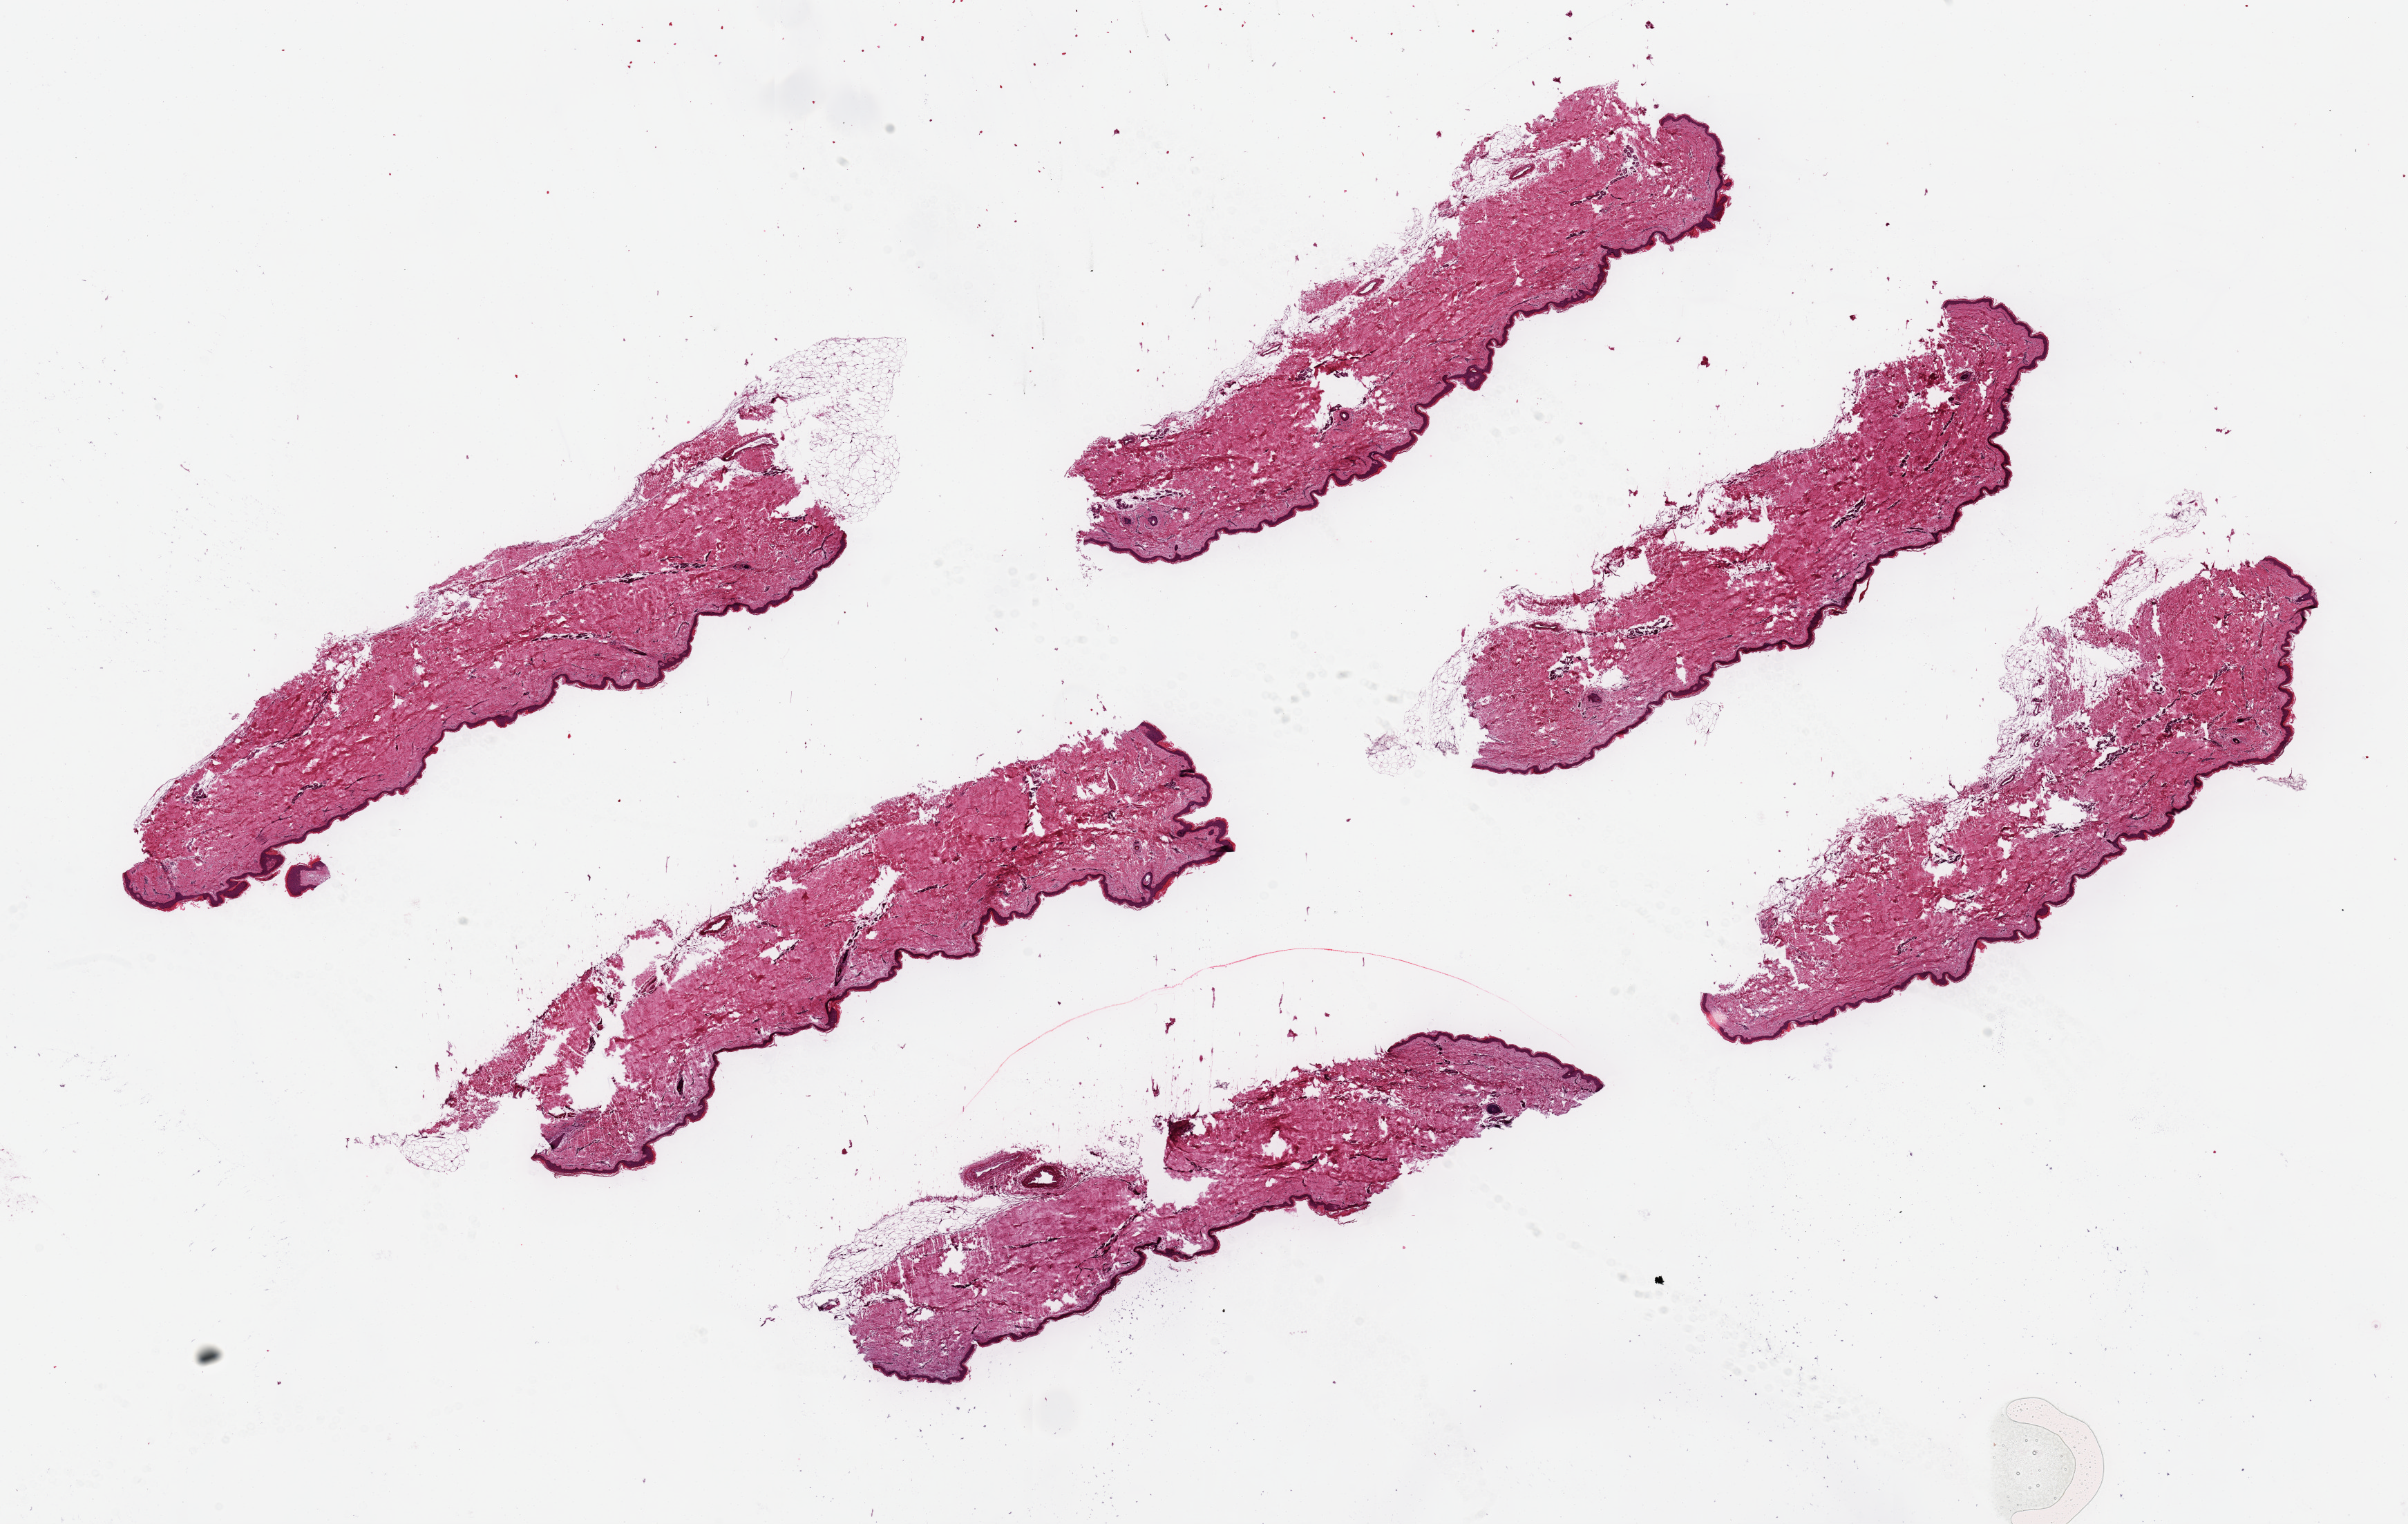
Whole-slide image, haematoxylin and eosin stain, a low-resolution overview of the entire scanned area, about 27.6 x 17.4 mm (slide scanned at 20x), PAXgene-fixed, paraffin-embedded tissue, section of skin of lower leg (target tissue), donor tissue sample. Female donor.
Reviewer comment on this tissue sample: 6 ~10x2 mm pieces. Severe fractured dermis, poorly fixed.